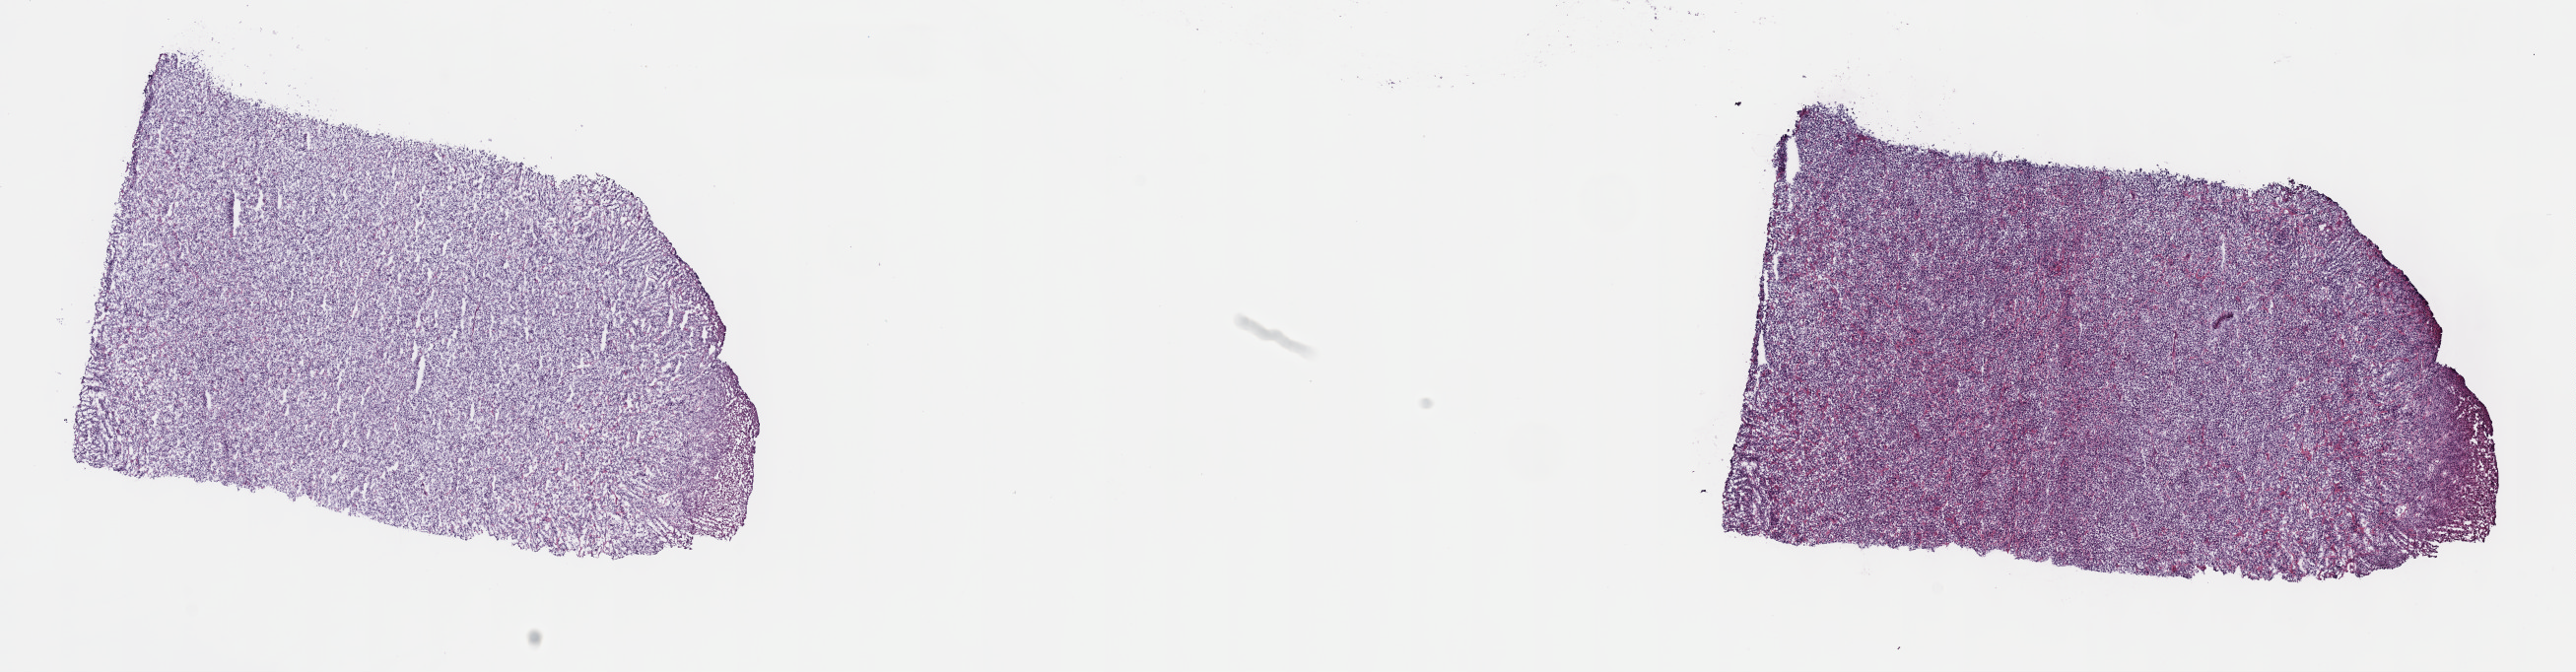
Digitized H&E tissue section (whole slide) — whole scanned area (about 21.1 x 5.5 mm, from a 40x scan) shown as a low-resolution overview, frozen section from the top of the tissue portion, lymphoid tissue, primary tumour sample. Male patient; age at initial diagnosis 51 years. Slide review estimates, as recorded: tumour cells 95%, tumour nuclei 95%, normal cells 0%, stromal cells 5%, necrosis 0%. Infiltration values recorded for this section: lymphocyte infiltration 90%, monocyte infiltration 5%, neutrophil infiltration 0%.
Diagnosis: Mediastinal (thymic) large B-cell lymphoma (lymph nodes of head, face and neck).